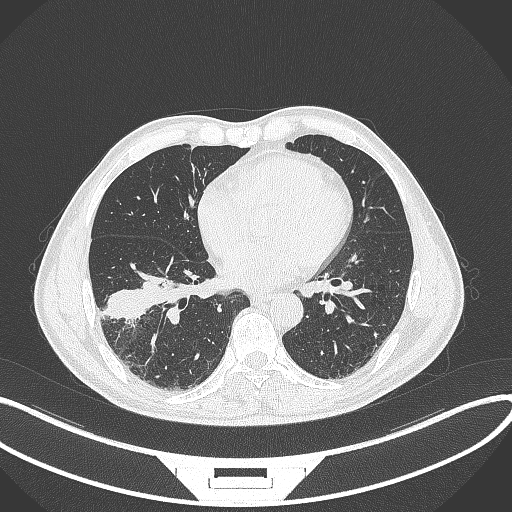
Chest CT, one axial slice; slice 147 of 364 in the series (ordered by position); reconstruction kernel B70f; 120 kVp; lung window (W 1500 / L -600 HU); 1 mm slice thickness; 512 × 512 image matrix, field of view 400 × 400 mm. Male patient, age 58 years. From the clinical record (not read from this slice): clinical TNM (as recorded): T3 N0 M0; histopathological grade: G2.
Structures marked on this image (rectangle marked by the reading radiologist):
- lung tumour (recorded histology: squamous cell carcinoma): bounding box [x1, y1, x2, y2] px = [107, 269, 180, 325]